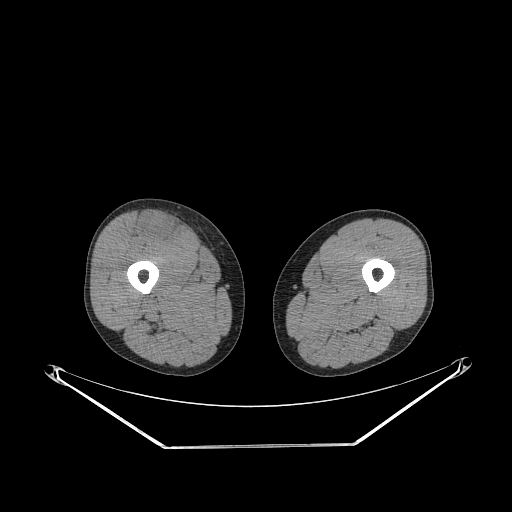
CT of an extremity soft-tissue mass (from a PET/CT study), one axial slice. Slice 253 of 311 in the series (ordered by position). 140 kVp. Soft-tissue window (W 400 / L 40 HU). 3.75 mm slice thickness. 512 × 512 image matrix, field of view 500 × 500 mm. Male patient. From the clinical record (not read from this slice): histological type: pleiomorphic leiomyosarcoma; grade: intermediate; site of the primary tumour: right thigh.
Structures marked on this image (expert contour drawn on MRI and transferred to this co-registered scan by the dataset authors):
- gross tumour volume including surrounding oedema: bounding box <141,212,179,241> (left, top, right, bottom; pixels)